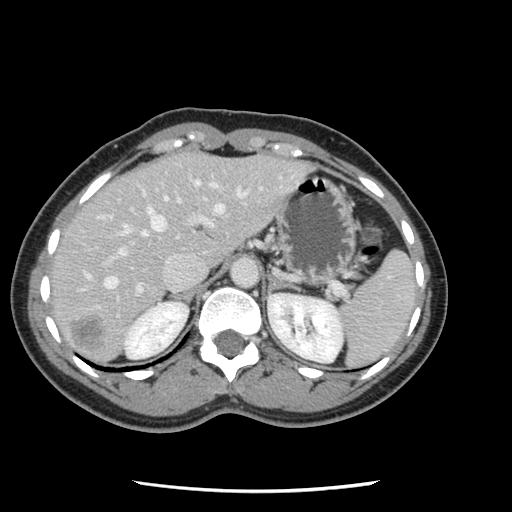
Contrast-enhanced abdominal CT, one axial slice. Slice 86 of 134 in the series (ordered by position). Intravenous contrast given. Soft-tissue window (W 400 / L 40 HU). 512 × 512 image matrix. Female patient, age 43 years. From the clinical record (not read from this slice): diagnosis: colorectal cancer liver metastases, imaged before liver resection; multiple liver metastases: yes.
Outlined on this slice (manually delineated by an expert):
- hepatic veins: bounding box (x1, y1, x2, y2) in pixels: (81, 180, 246, 290)
- liver: (50, 153, 307, 364)
- planned liver remnant (the part of the liver to remain after resection): (50, 156, 190, 309)
- portal vein (with intrahepatic branches): (96, 181, 261, 316)
- liver metastasis: (71, 315, 106, 349)